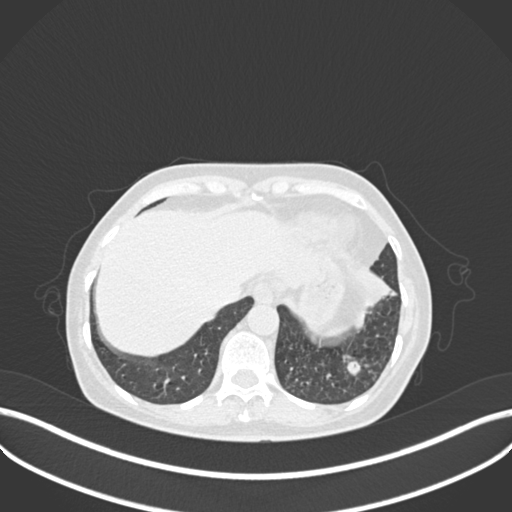
Chest CT, one axial slice. Position 46 of 270 along the scan axis. 120 kVp. Lung window (W 1500 / L -600 HU). 1 mm slice thickness. 512 × 512 image matrix. Patient: female, 63 years. From the clinical record (not read from this slice): clinical TNM (as recorded): T1b N0 M0; histopathological grade: G2-3.
Outlined on this slice (rectangle marked by the reading radiologist):
- lung tumour (recorded histology: adenocarcinoma): bounding box (x1, y1, x2, y2) in pixels: (355, 268, 404, 314)